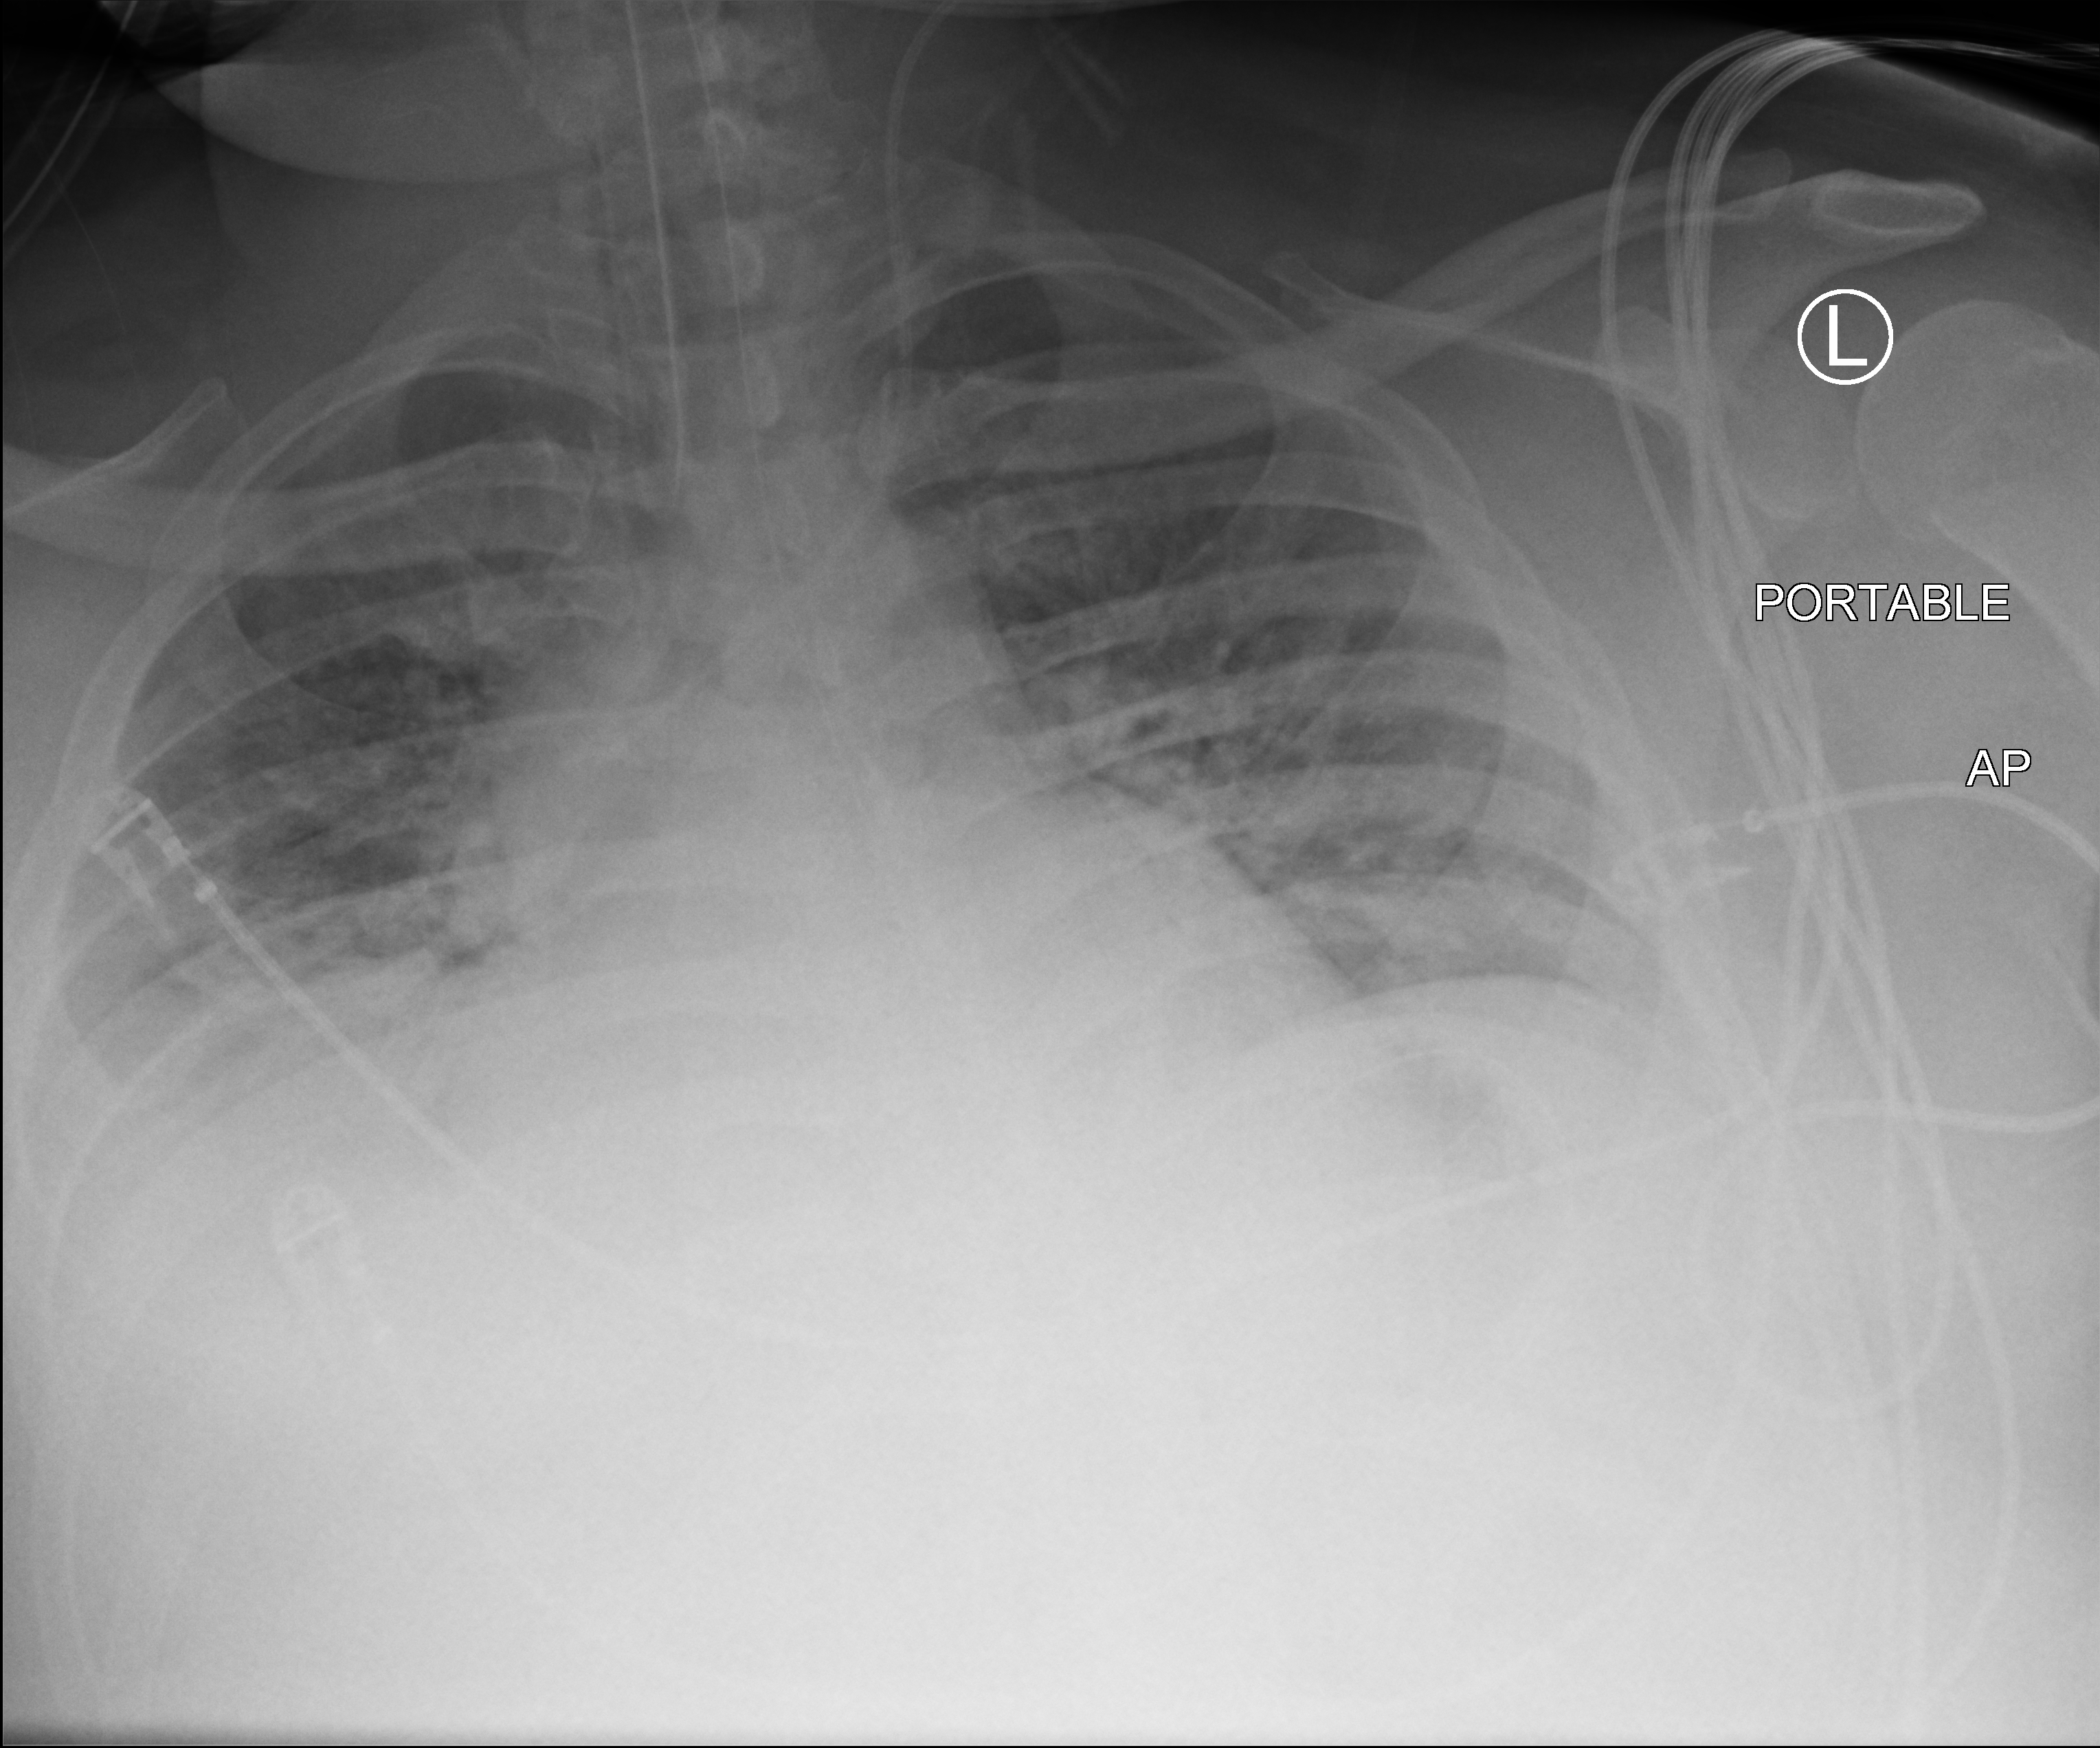
Chest X-ray (portable); anteroposterior (AP) projection. Male patient hospitalised with COVID-19, age 18–59 years.
Admission-level facts for this patient (not findings on this image; timing relative to this image not recorded): admitted to intensive care during this hospital stay: yes.